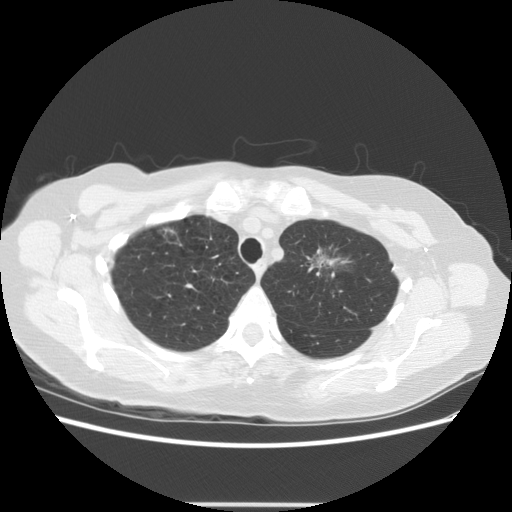
Axial slice from a low-dose chest CT screening exam. Third screening round (two years after baseline). Lung window (W 1500 / L -600 HU). 2.5 mm slice thickness. Standard (soft-tissue) reconstruction kernel (STANDARD). Slice 102 of 126 in the series. 512 × 512 image matrix, field of view 360 × 360 mm. Female, age 65 years at enrolment. Former smoker at enrolment.
Expert-annotated lung lesion, bounding box <291,228,368,294> (left, top, right, bottom; pixels). Reader record for this screening exam (exam-level; its link to the box is not recorded): non-calcified nodule or mass ≥4 mm, left upper lobe, 17 × 14 mm, poorly defined margins, ground glass attenuation, pre-existing on the prior screen: yes; interval growth: yes. Lung cancer was diagnosed 96 days after this screen: adenocarcinoma, NOS, left upper lobe, moderately differentiated (G2), stage IA (AJCC 6th edition), 30 mm at pathology.